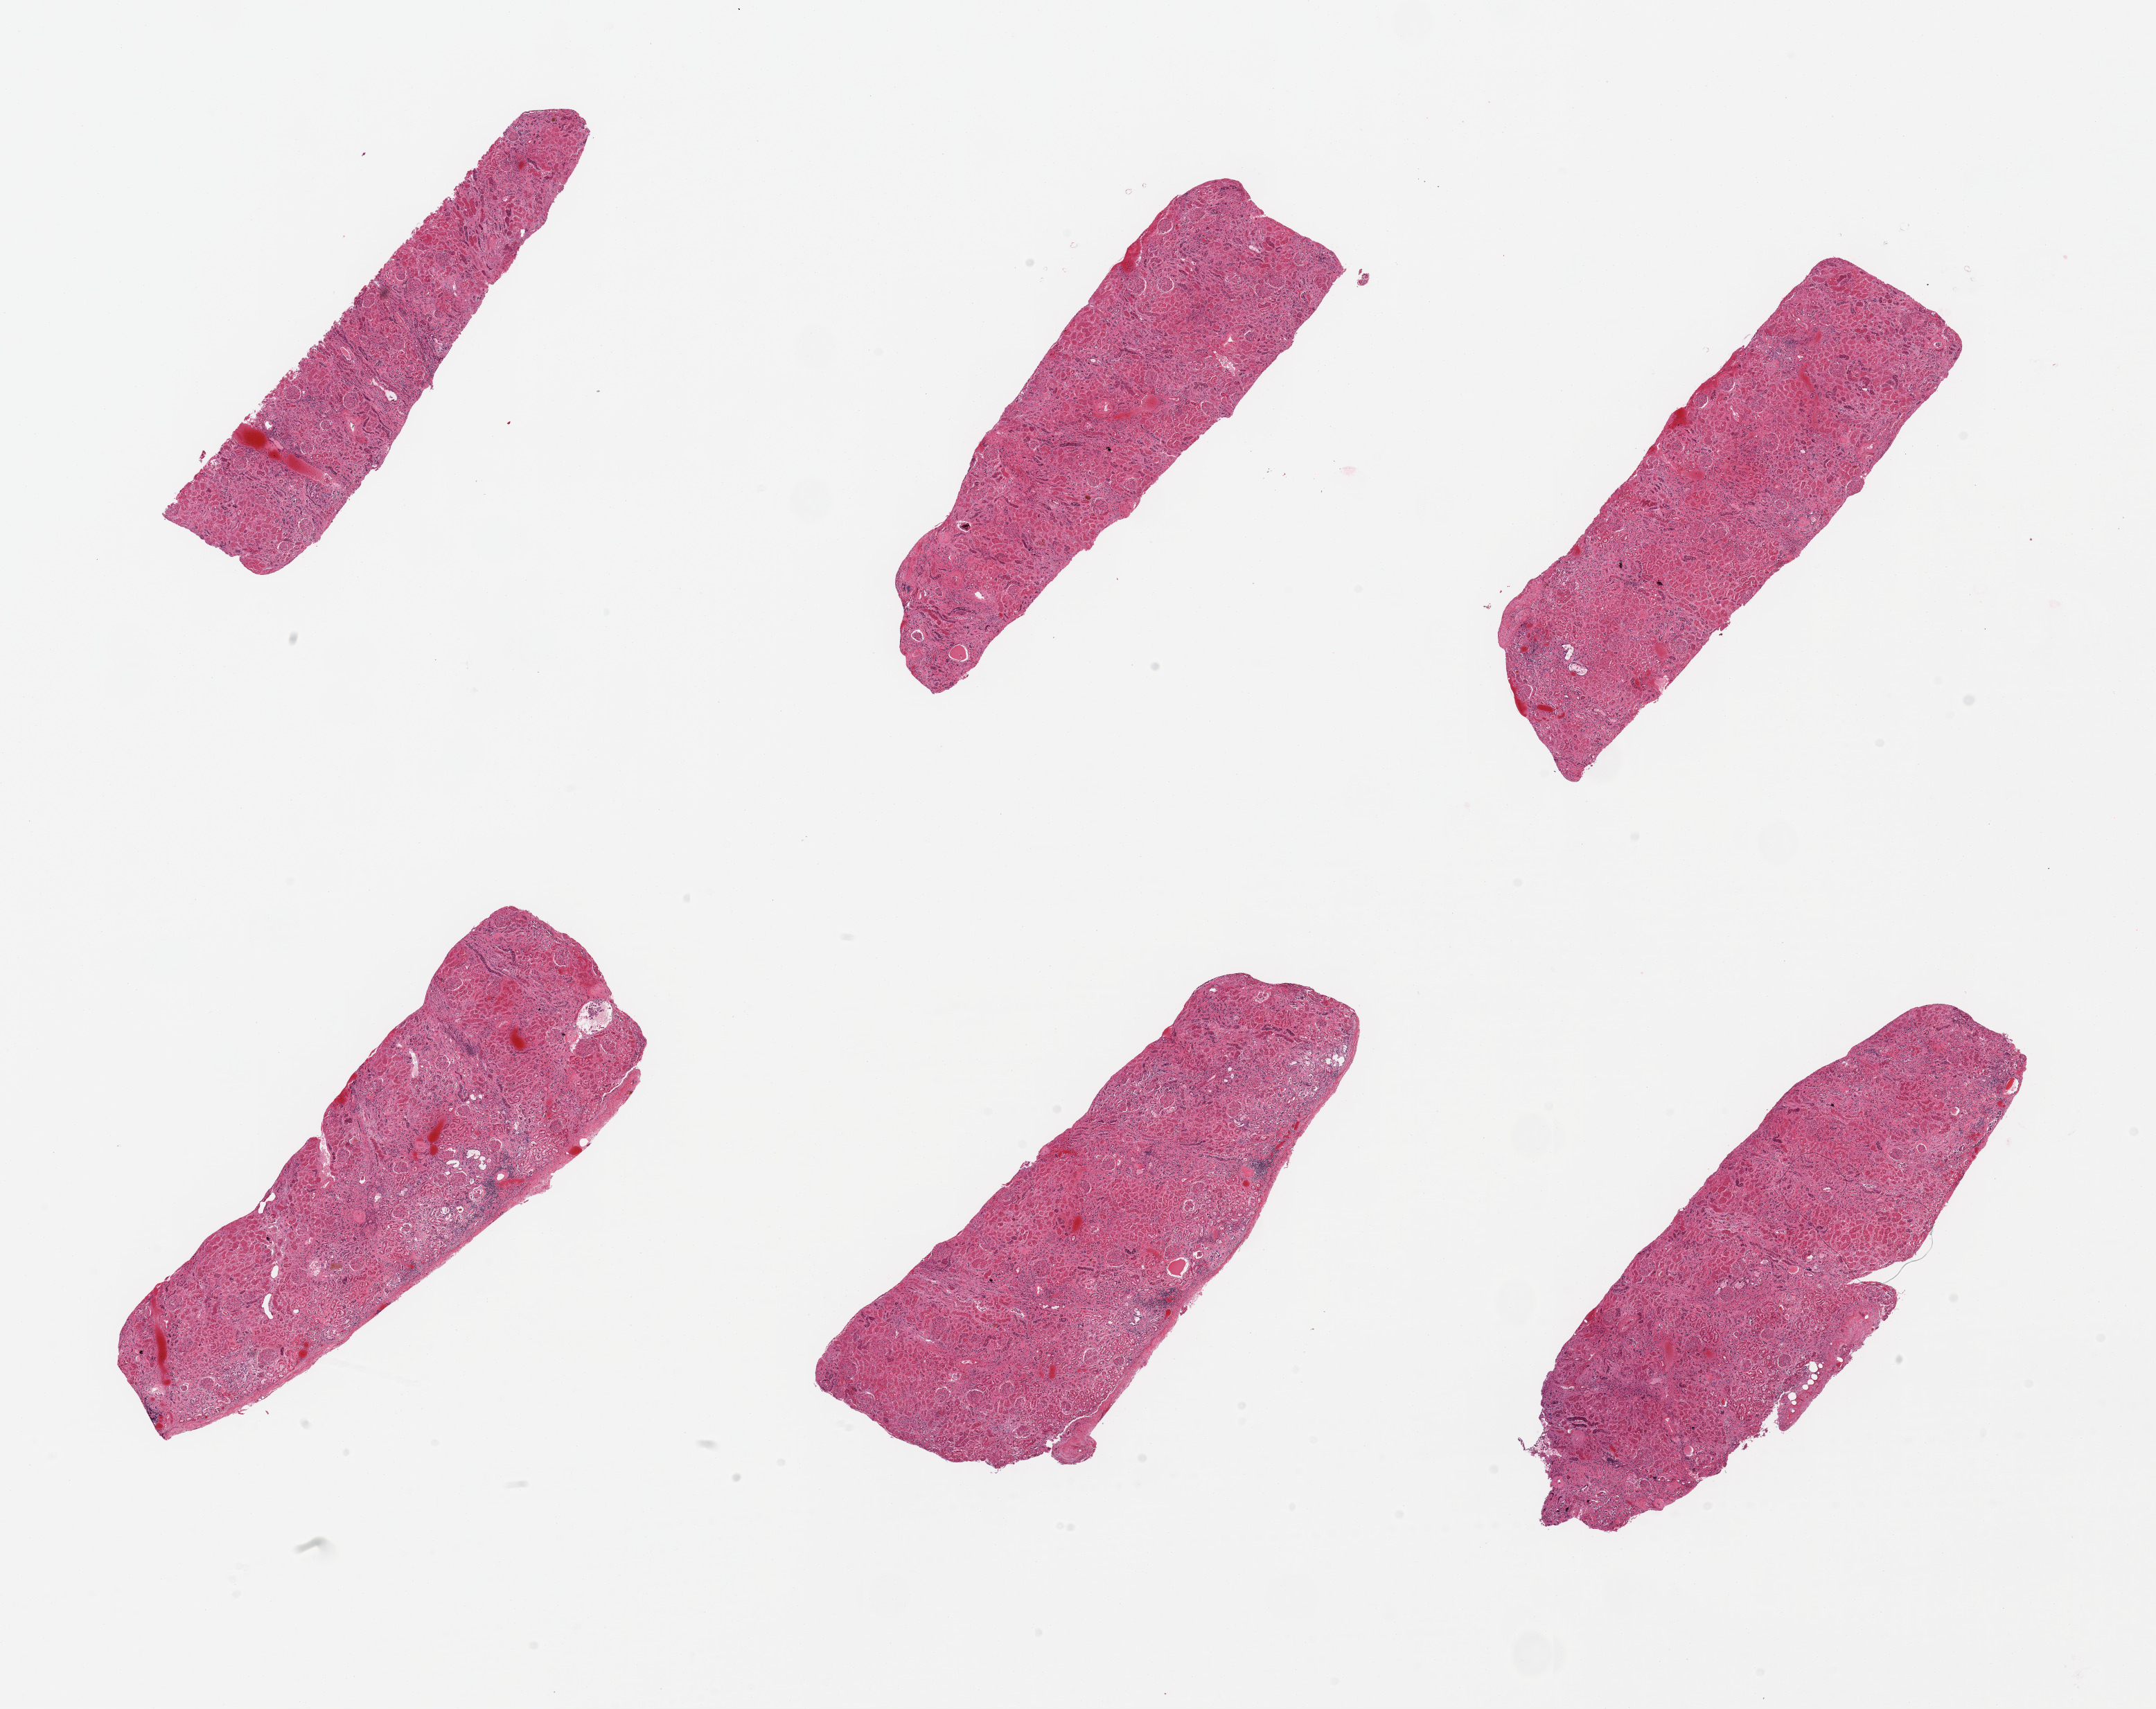
Hematoxylin and eosin (H&E) whole-slide image — low-resolution overview of the scanned area, about 24.6 x 19.5 mm (slide scanned at 20x), PAXgene-fixed paraffin-embedded (PFPE) section, section of renal cortex (target tissue), tissue donor sample. Female donor.
Review note (as recorded): 6 pieces; tubules severely autolyzed; scattered sclerosed glomeruli; small foci of lymphoid cells.